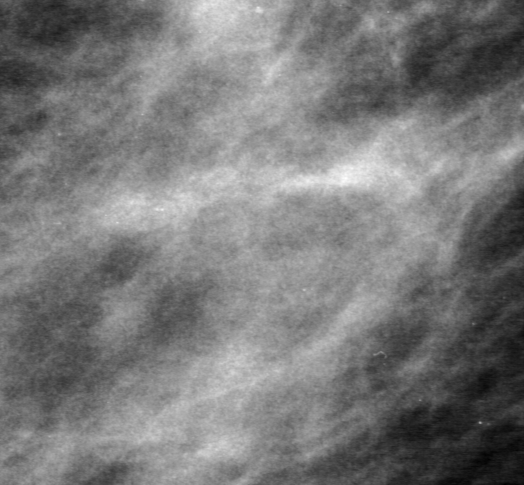
Region of interest cut from a scanned film mammogram (one marked finding); right breast; MLO view.
Mass, shape architectural distortion; BI-RADS assessment category 0 (incomplete: needs additional imaging); pathology result (as recorded, not read from the image): malignant.